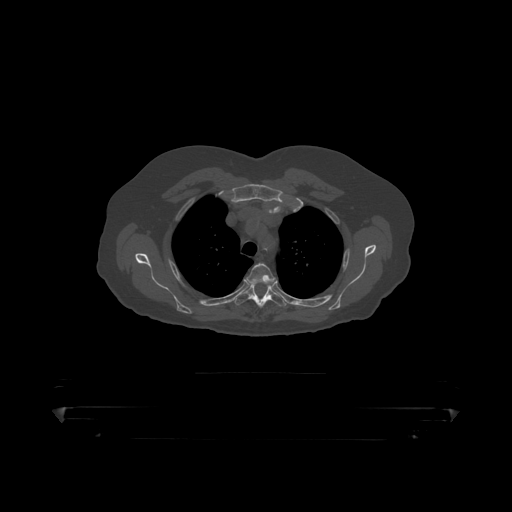
CT including the spine, one axial slice; slice 347 of 390 in the series (ordered by position); reconstruction kernel STANDARD; 120 kVp; bone window (W 1800 / L 400 HU); 512 × 512 image matrix, field of view 650 × 650 mm. Patient: male, 60 years. From the clinical record (not read from this slice): primary cancer: prostate.
Annotated regions visible in this slice (semi-automatically segmented with operator editing):
- T3 vertebra: bounding box (x1, y1, x2, y2) in pixels: (247, 264, 276, 286)
- T4 vertebra: (235, 284, 287, 310)